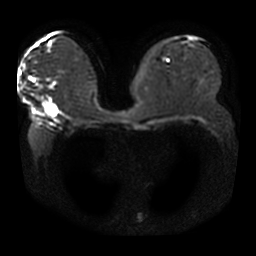
Breast MRI, one axial slice. Slice 21 of 42 in the series (ordered by position). Diffusion-weighted series; image 2 of 4 stored at this slice position (different b-values; order by instance number). 3 T. 5 mm slice thickness. 256 × 256 image matrix, field of view 360 × 360 mm. Female patient.
Annotated regions visible in this slice (outlined manually by an expert reader):
- tumour on diffusion-weighted imaging: bounding box (x1, y1, x2, y2) in pixels: (44, 103, 58, 116)